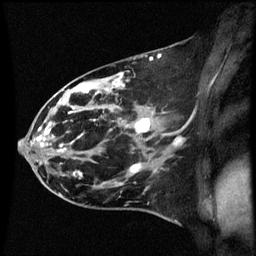
Breast MRI (dynamic contrast-enhanced), one sagittal slice; slice 30 of 60 in the series (ordered by position); dynamic contrast-enhanced series, image 2 of 3 at this slice position (ordered by acquisition); 1.5 T; TE 4.2 ms, TR 8.9 ms; 256 × 256 image matrix, field of view 200 × 200 mm. Female patient, age 44 years. Case-level facts recorded for this patient, not image findings: setting: breast cancer imaged before/during neoadjuvant chemotherapy; receptor status: HR-positive, HER2-negative.
Structures marked on this image (semi-automatic segmentation, software-assisted and operator-edited):
- analysis volume of interest (the breast-tissue region the enhancement analysis was run in; not a lesion): box from (x=43, y=78) to (x=153, y=189) px
- tumour enhancement mask (voxels above the 70 % enhancement threshold inside the analysis volume of interest): (x=50, y=78)–(x=150, y=177)